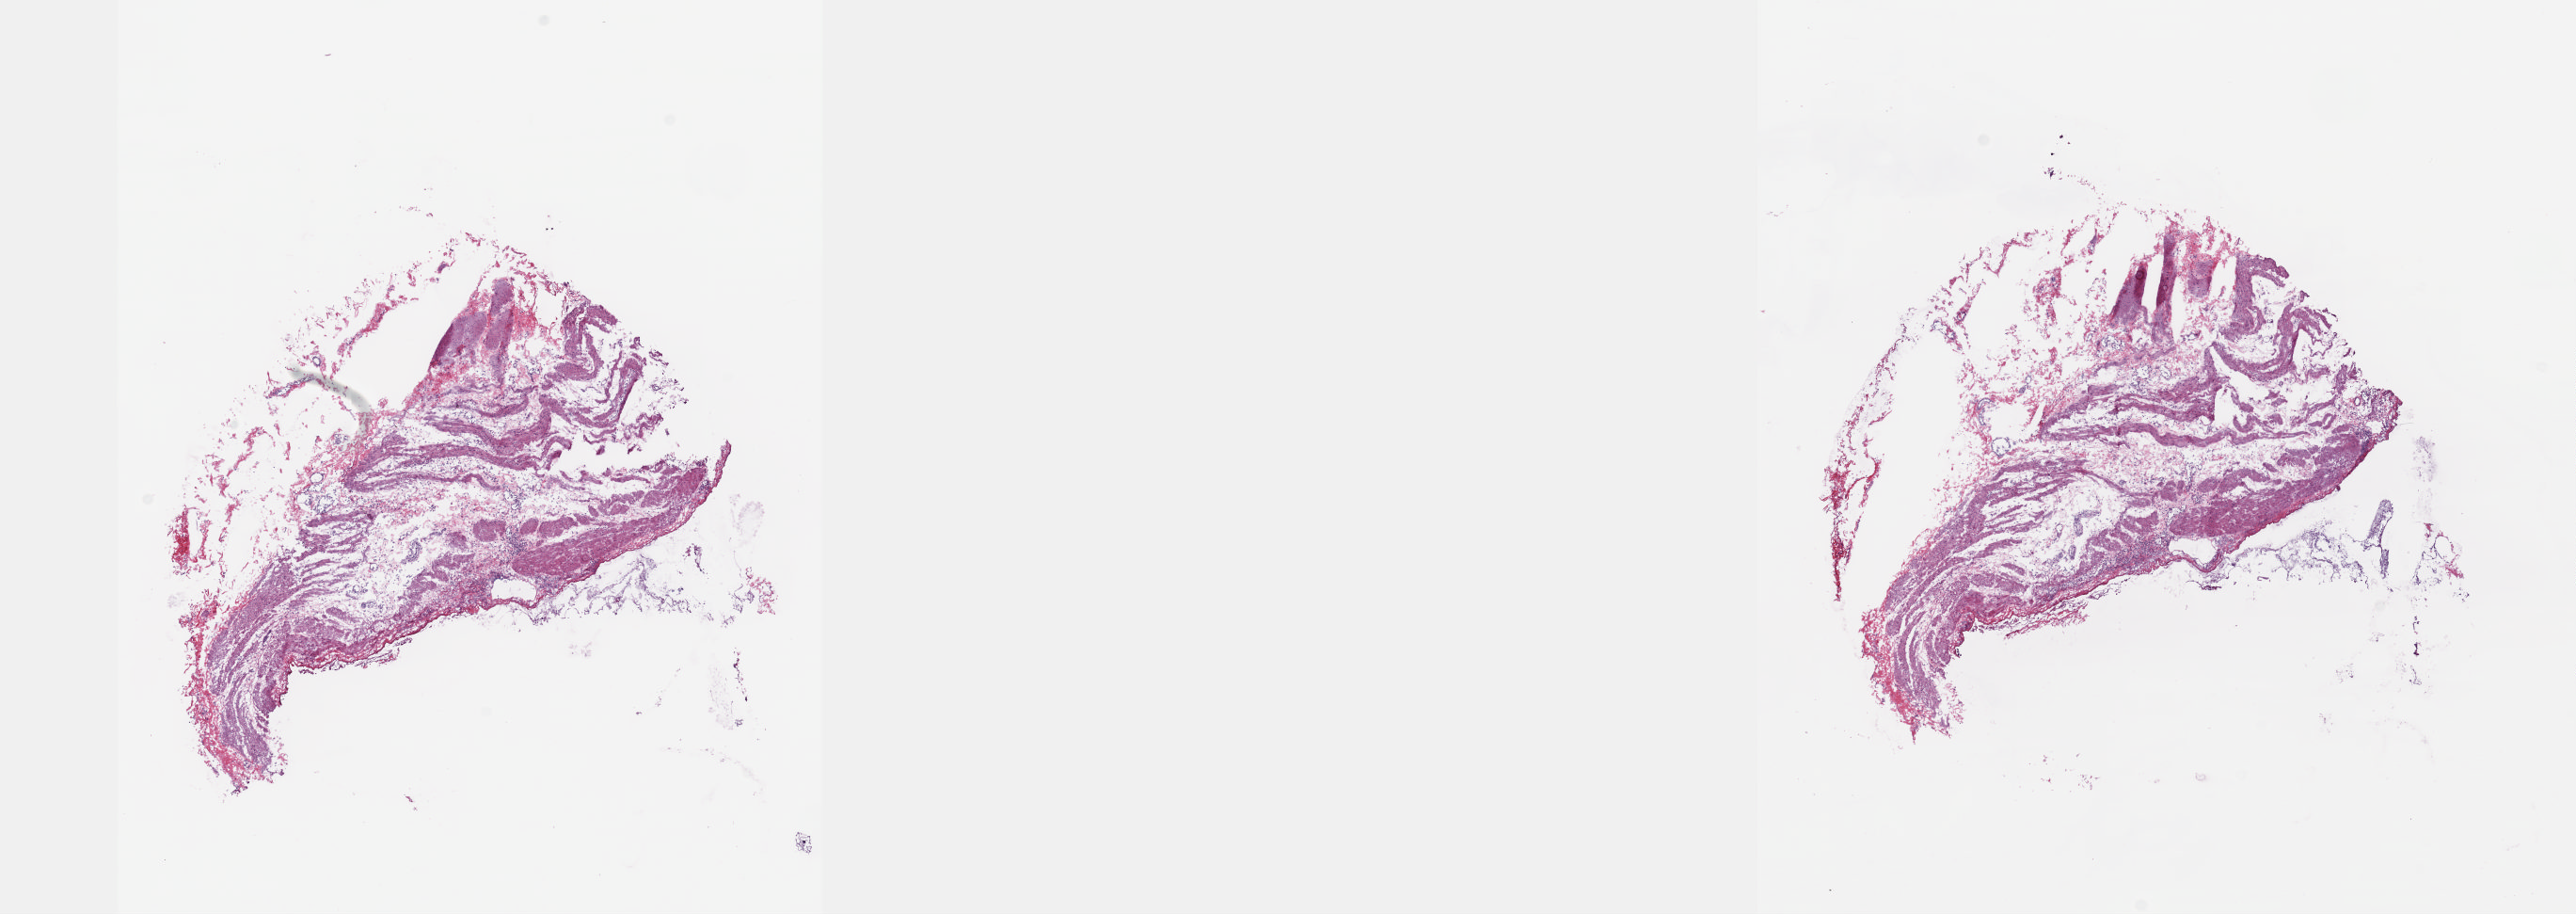
Whole-slide histology image, H&E-stained — a low-resolution overview of the entire scanned area, about 22.1 x 7.8 mm (acquisition: 20x scan), frozen section from the top of the tissue portion, solid tissue normal (non-tumour tissue) sample from the esophagus. Patient: male, age at initial diagnosis 51 years. Composition of this section per pathologist review: tumour cells 0%, tumour nuclei 0%, normal cells 100%, stromal cells 0%, necrosis 0%. Infiltration values recorded for this section: lymphocyte infiltration 0%, monocyte infiltration 0%, neutrophil infiltration 0%.
This section: solid tissue normal (non-tumour) sample from the same patient. Patient diagnosis: Adenocarcinoma, NOS (lower third of esophagus).